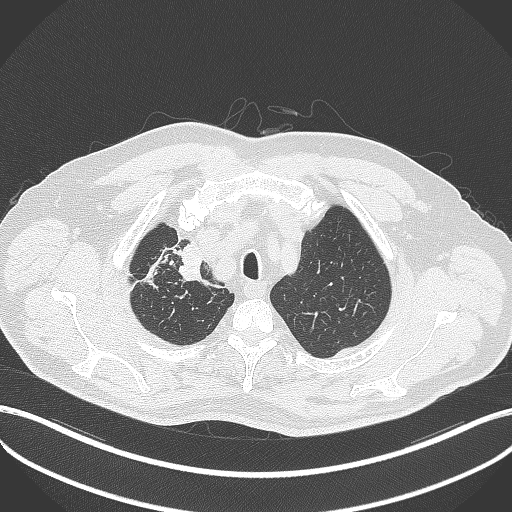
Chest CT, one axial slice. Slice 330 of 411 in the series (ordered by position). Reconstruction kernel B70f. Lung window (W 1500 / L -600 HU). 1 mm slice thickness. 512 × 512 image matrix, field of view 400 × 400 mm. Patient: male, 60 years. From the clinical record (not read from this slice): clinical TNM (as recorded): T1b N1 M0.
Structures marked on this image (rectangle marked by the reading radiologist):
- lung tumour (recorded histology: squamous cell carcinoma): bounding box [x1, y1, x2, y2] px = [174, 243, 227, 296]